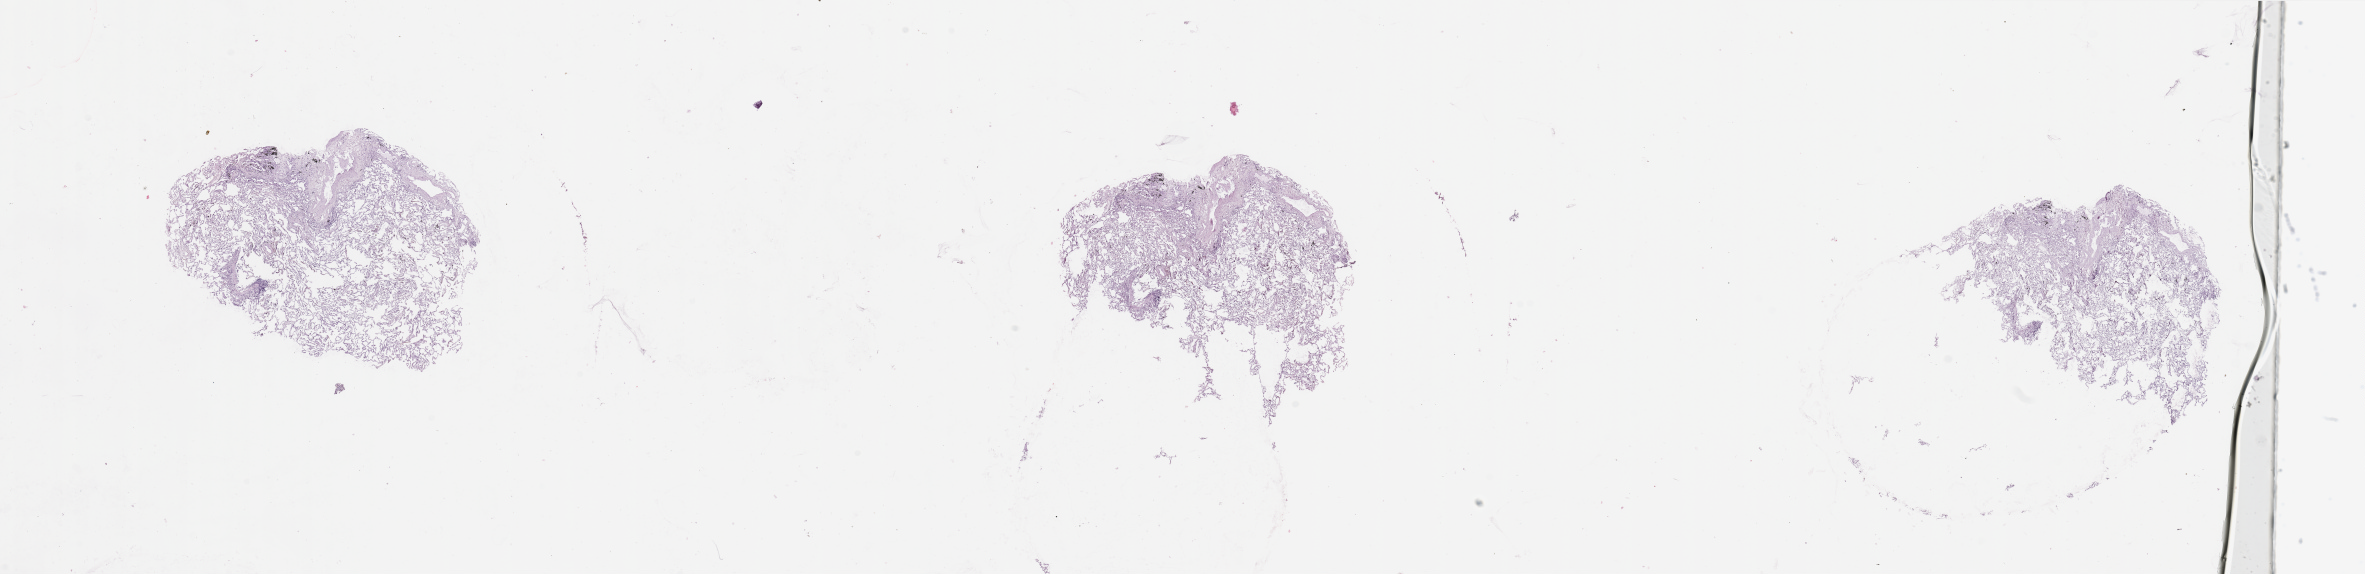
Whole-slide histology image, Hematoxylin and eosin (H&E) stained — shown as a low-resolution overview of the whole scanned area (about 37.4 x 9.1 mm); normal (non-tumour) tissue sample, sampled site: lung. Patient: male, age 76 years.
This section: normal (non-tumour) tissue from the same patient. Patient diagnosis: Adenocarcinoma, NOS.